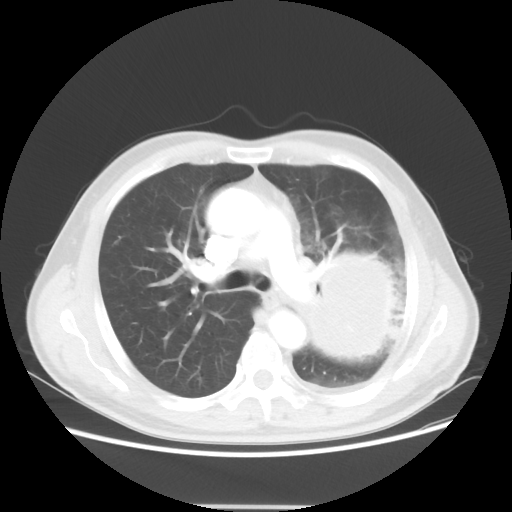
Chest CT, one axial slice; slice 34 of 53 in the series (ordered by position); lung window (W 1500 / L -600 HU); 512 × 512 image matrix. Patient: male, 60 years. Case-level facts recorded for this patient, not image findings: clinical TNM (as recorded): T4 N1 M1a; histopathological grade: G3.
Annotated regions visible in this slice (bounding box drawn by a radiologist):
- lung tumour (recorded histology: large cell carcinoma): bounding box [x1, y1, x2, y2] px = [298, 241, 413, 383]